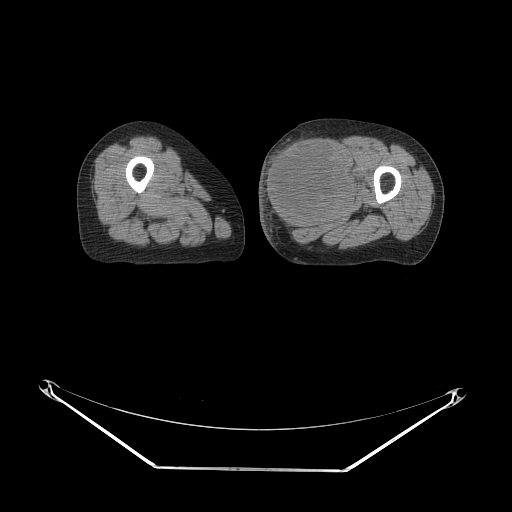
CT of an extremity soft-tissue mass (from a PET/CT study), one axial slice; slice 32 of 91 in the series (ordered by position); reconstruction kernel STANDARD; 140 kVp; soft-tissue window (W 400 / L 40 HU); 512 × 512 image matrix, field of view 500 × 500 mm. Female patient. From the clinical record (not read from this slice): histological type: pleomorphic leiomyosarcoma; grade: high; site of the primary tumour: left thigh.
Structures marked on this image (expert contour drawn on MRI and transferred to this co-registered scan by the dataset authors):
- gross tumour volume including surrounding oedema: bounding box [x1, y1, x2, y2] px = [263, 132, 355, 229]
- gross tumour volume (mass): [263, 135, 353, 227]